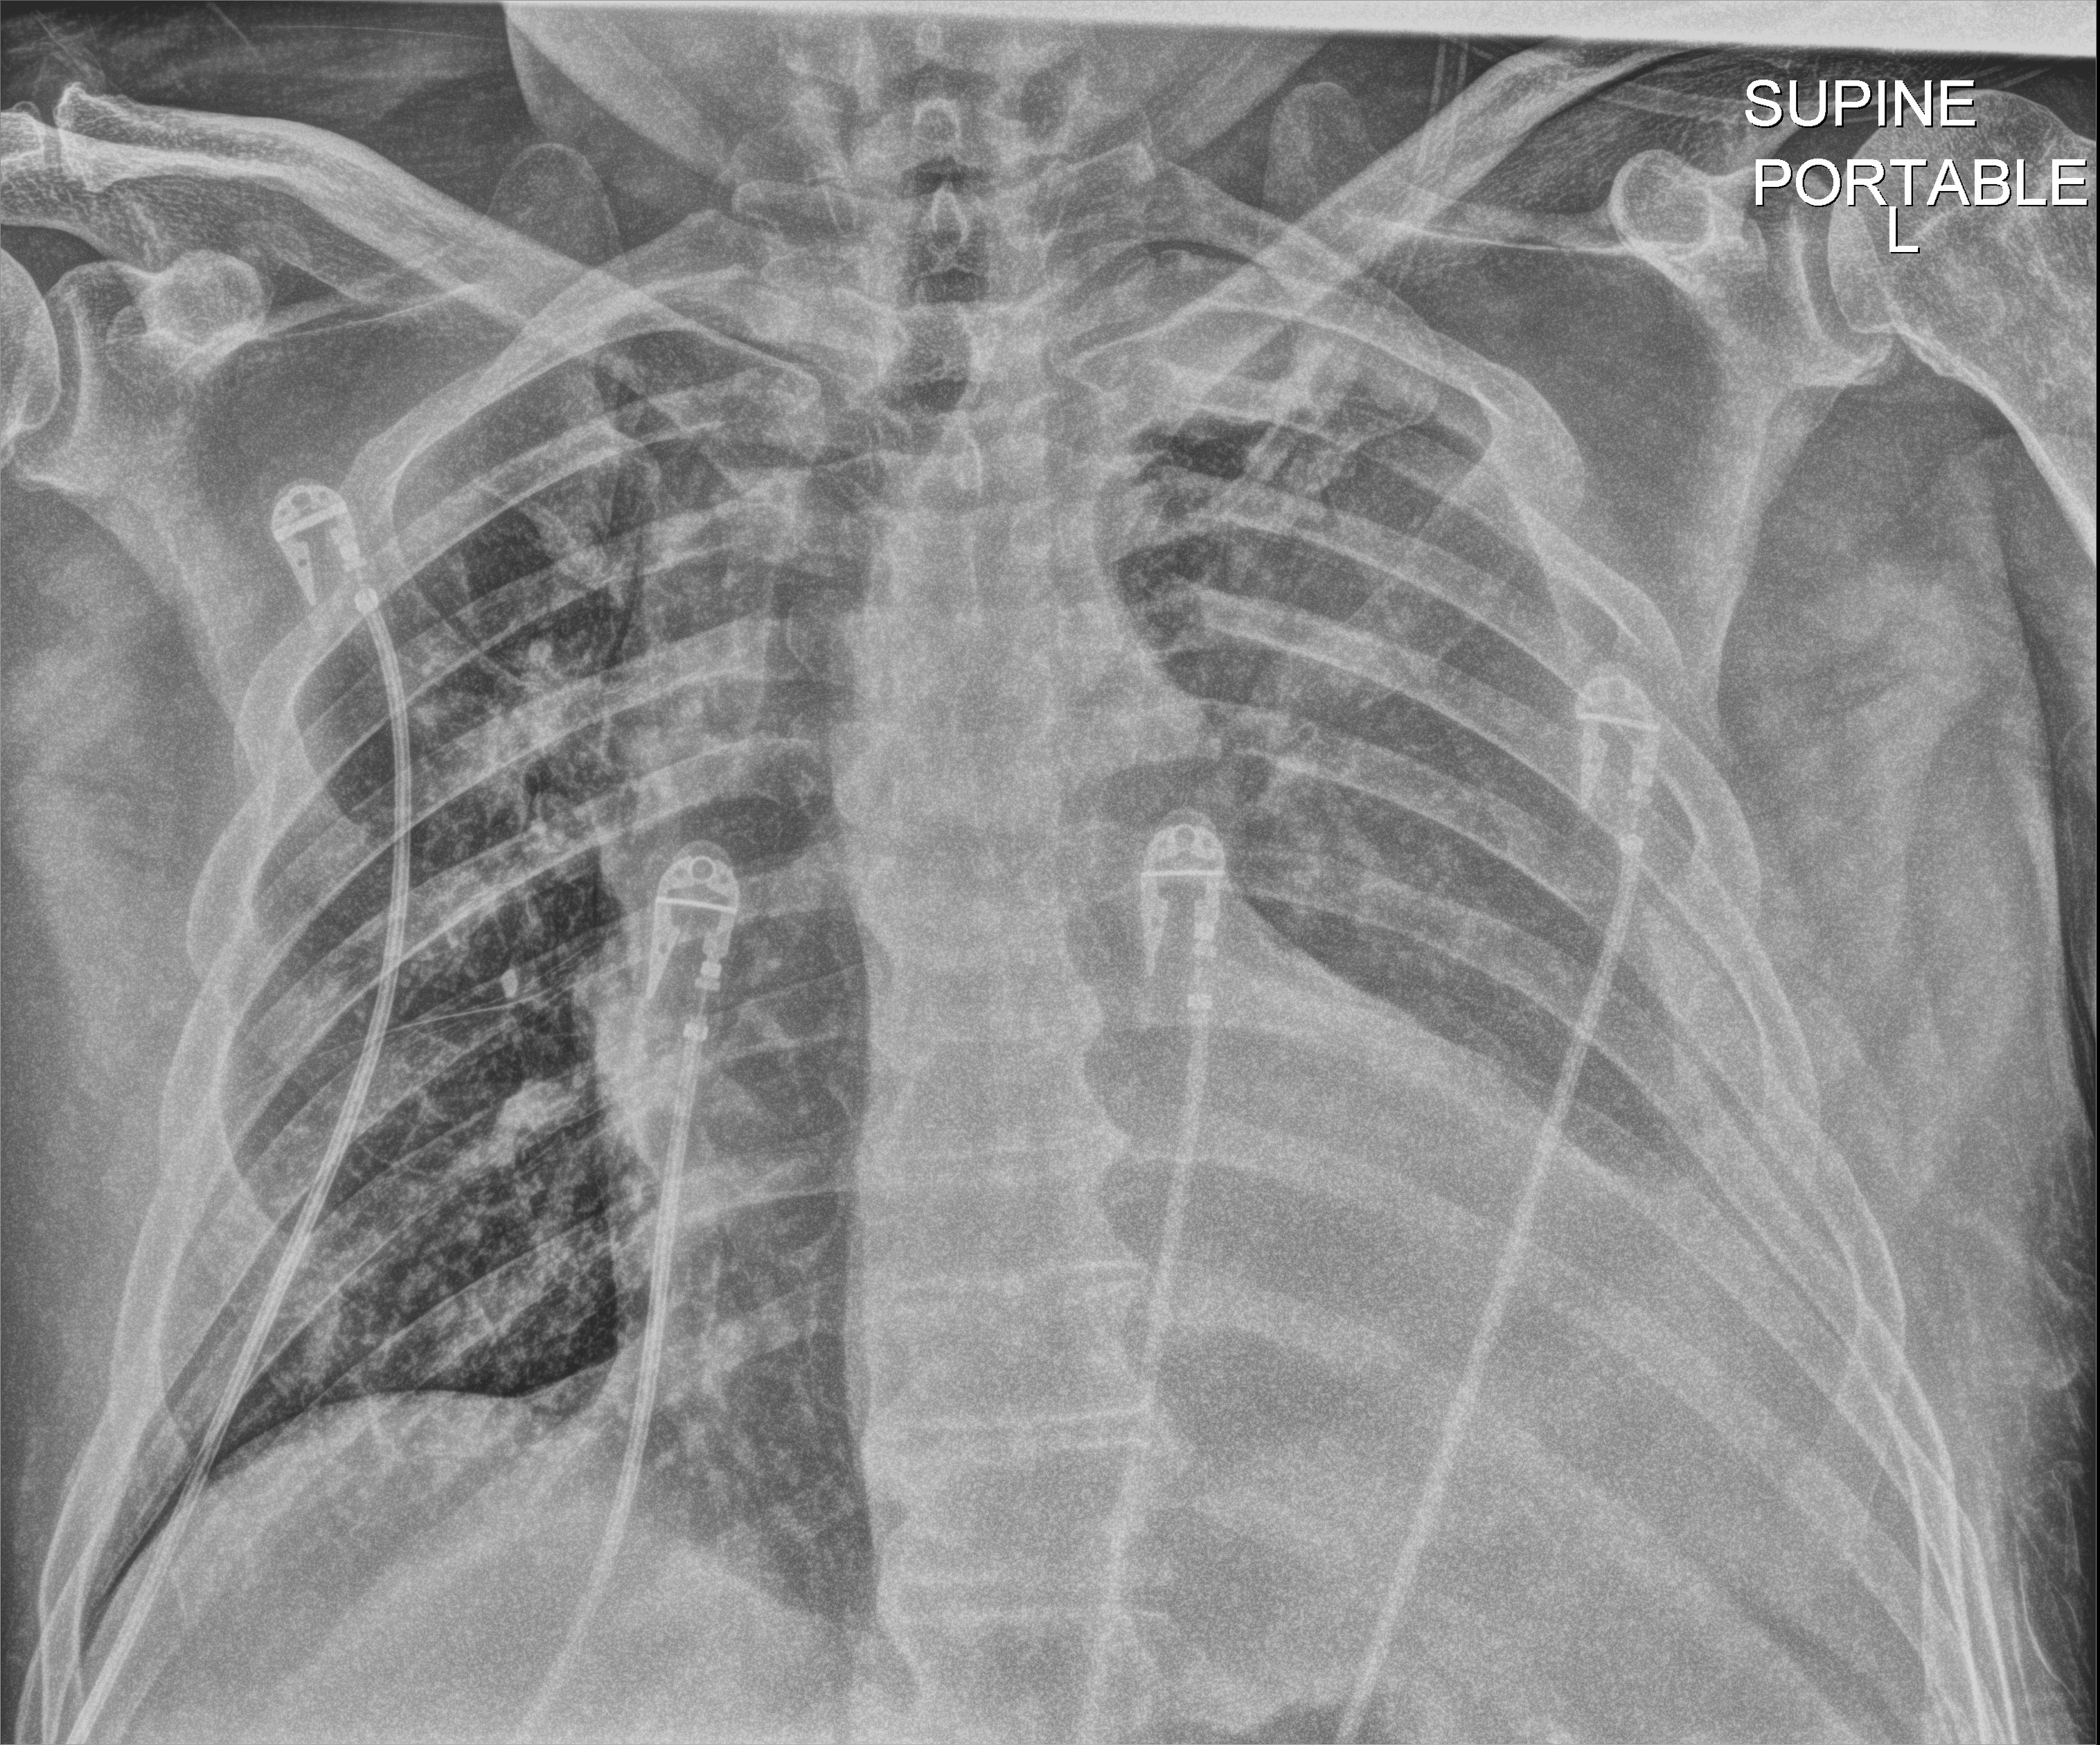
Chest X-ray (portable), anteroposterior (AP) projection. Male patient hospitalised with COVID-19, age 18–59 years.
Admission-level facts for this patient (not findings on this image; timing relative to this image not recorded):
- mechanically ventilated during this hospital stay: no
- admitted to intensive care during this hospital stay: no